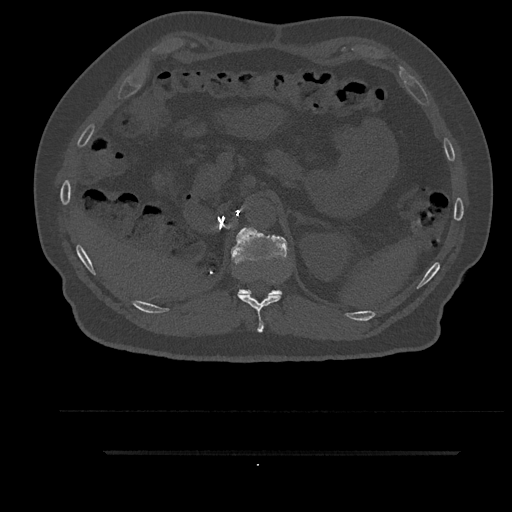
CT including the spine, one axial slice. Position 275 of 797 along the scan axis. 120 kVp. Bone window (W 1800 / L 400 HU). 0.5 mm slice thickness. 512 × 512 image matrix, field of view 432 × 432 mm. Male patient, age 63 years. Case-level facts recorded for this patient, not image findings: primary cancer: renal; vertebrae with lytic lesions (as recorded): T8.
Annotated regions visible in this slice (semi-automatically segmented with operator editing):
- T11 vertebra: bounding box (x1, y1, x2, y2) in pixels: (238, 294, 282, 333)
- T12 vertebra: (231, 227, 288, 295)